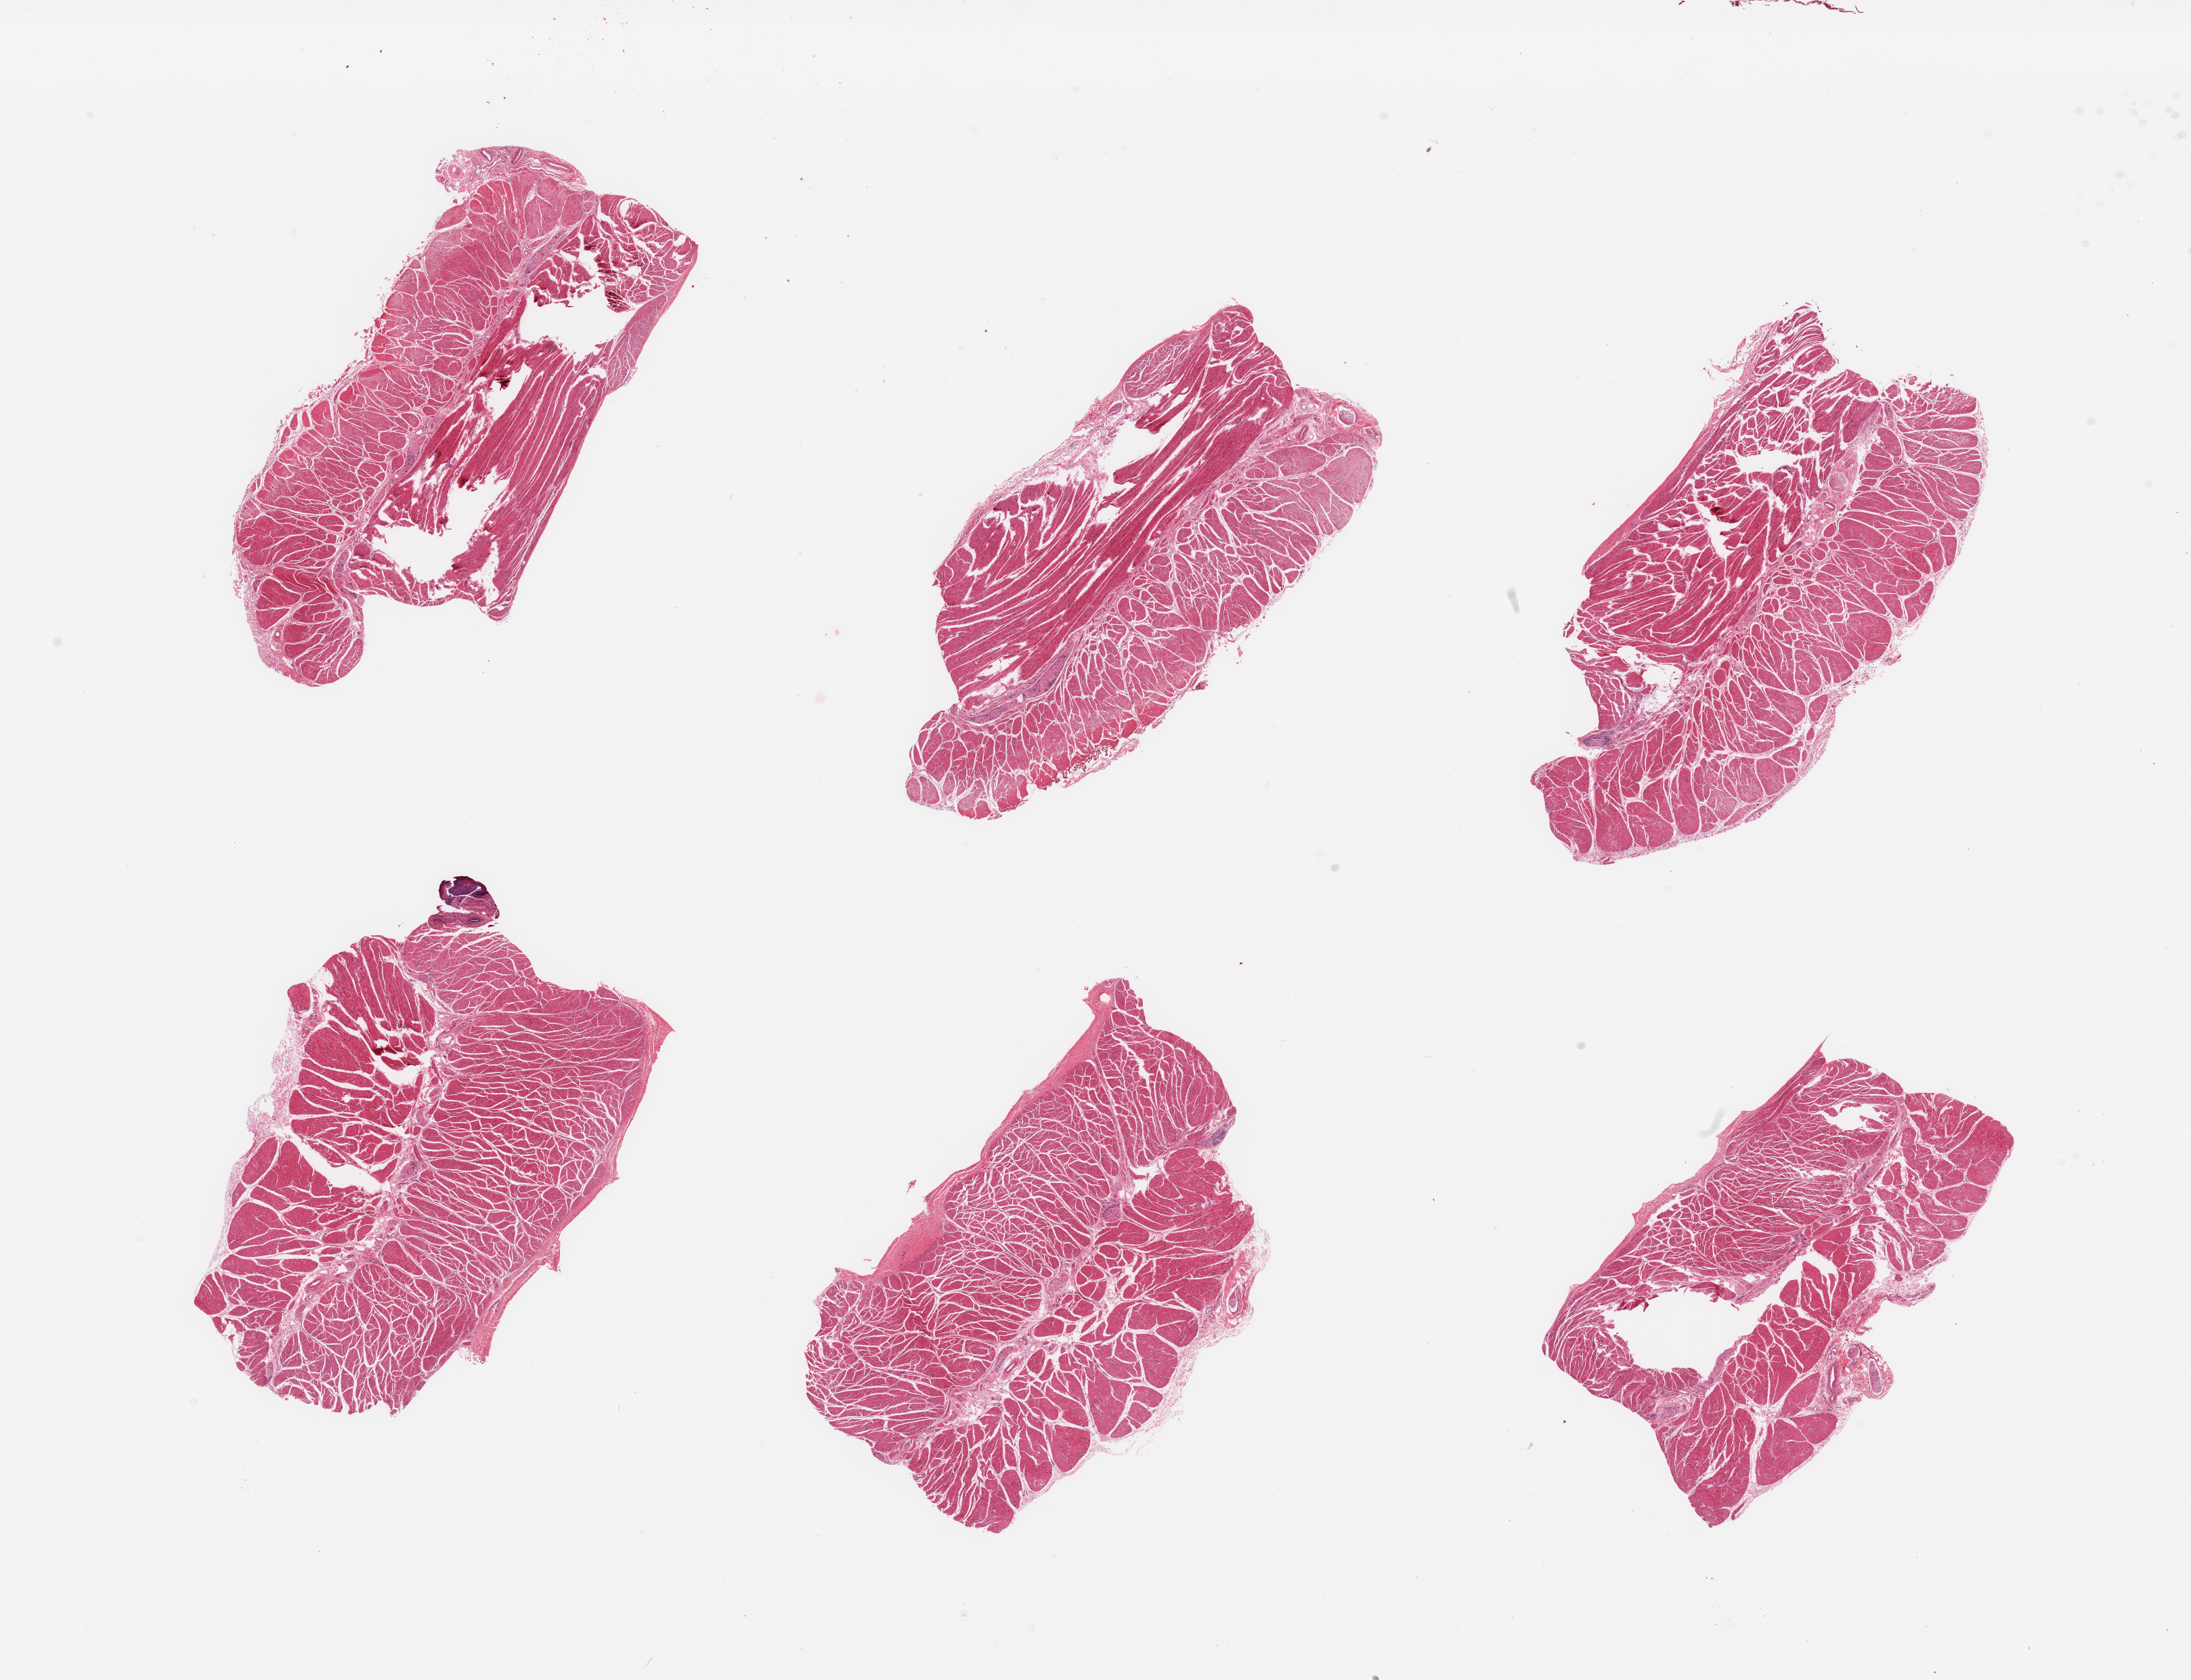
Hematoxylin and eosin (H&E) whole-slide image — a low-resolution overview of the entire scanned area, about 25.6 x 19.6 mm, PAXgene-fixed, paraffin-embedded tissue, section of esophageal muscle (target tissue), donor tissue sample. Male donor.
Reviewer comment on this tissue sample: 6 pieces; target muscularis.